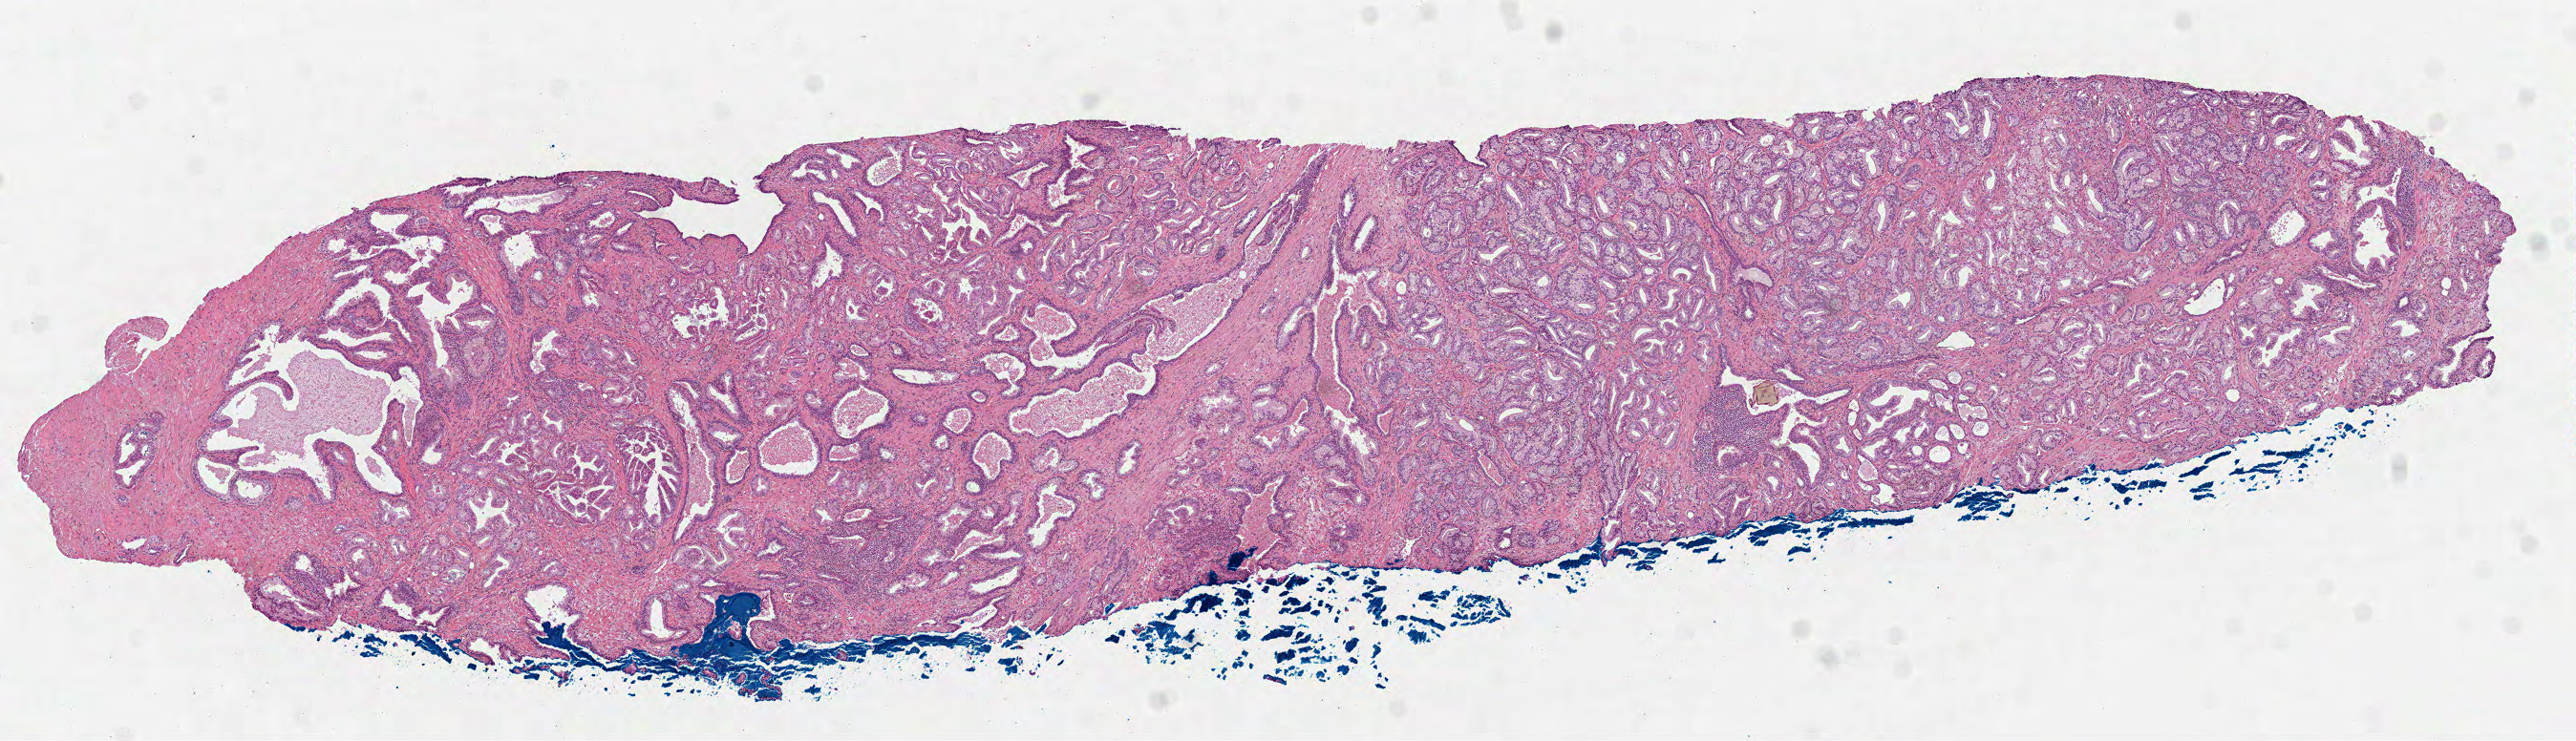
Digitized Hematoxylin and eosin (H&E) stained tissue section (whole slide), shown as a low-resolution overview of the whole scanned area (about 10.9 x 3.1 mm, acquisition: 40x scan); formalin-fixed paraffin-embedded (FFPE) diagnostic section; prostate, primary tumour sample. Male, age 64 years at initial diagnosis. Gleason score: 6 (3+3).
Pathologic diagnosis: Acinar cell carcinoma (prostate gland).